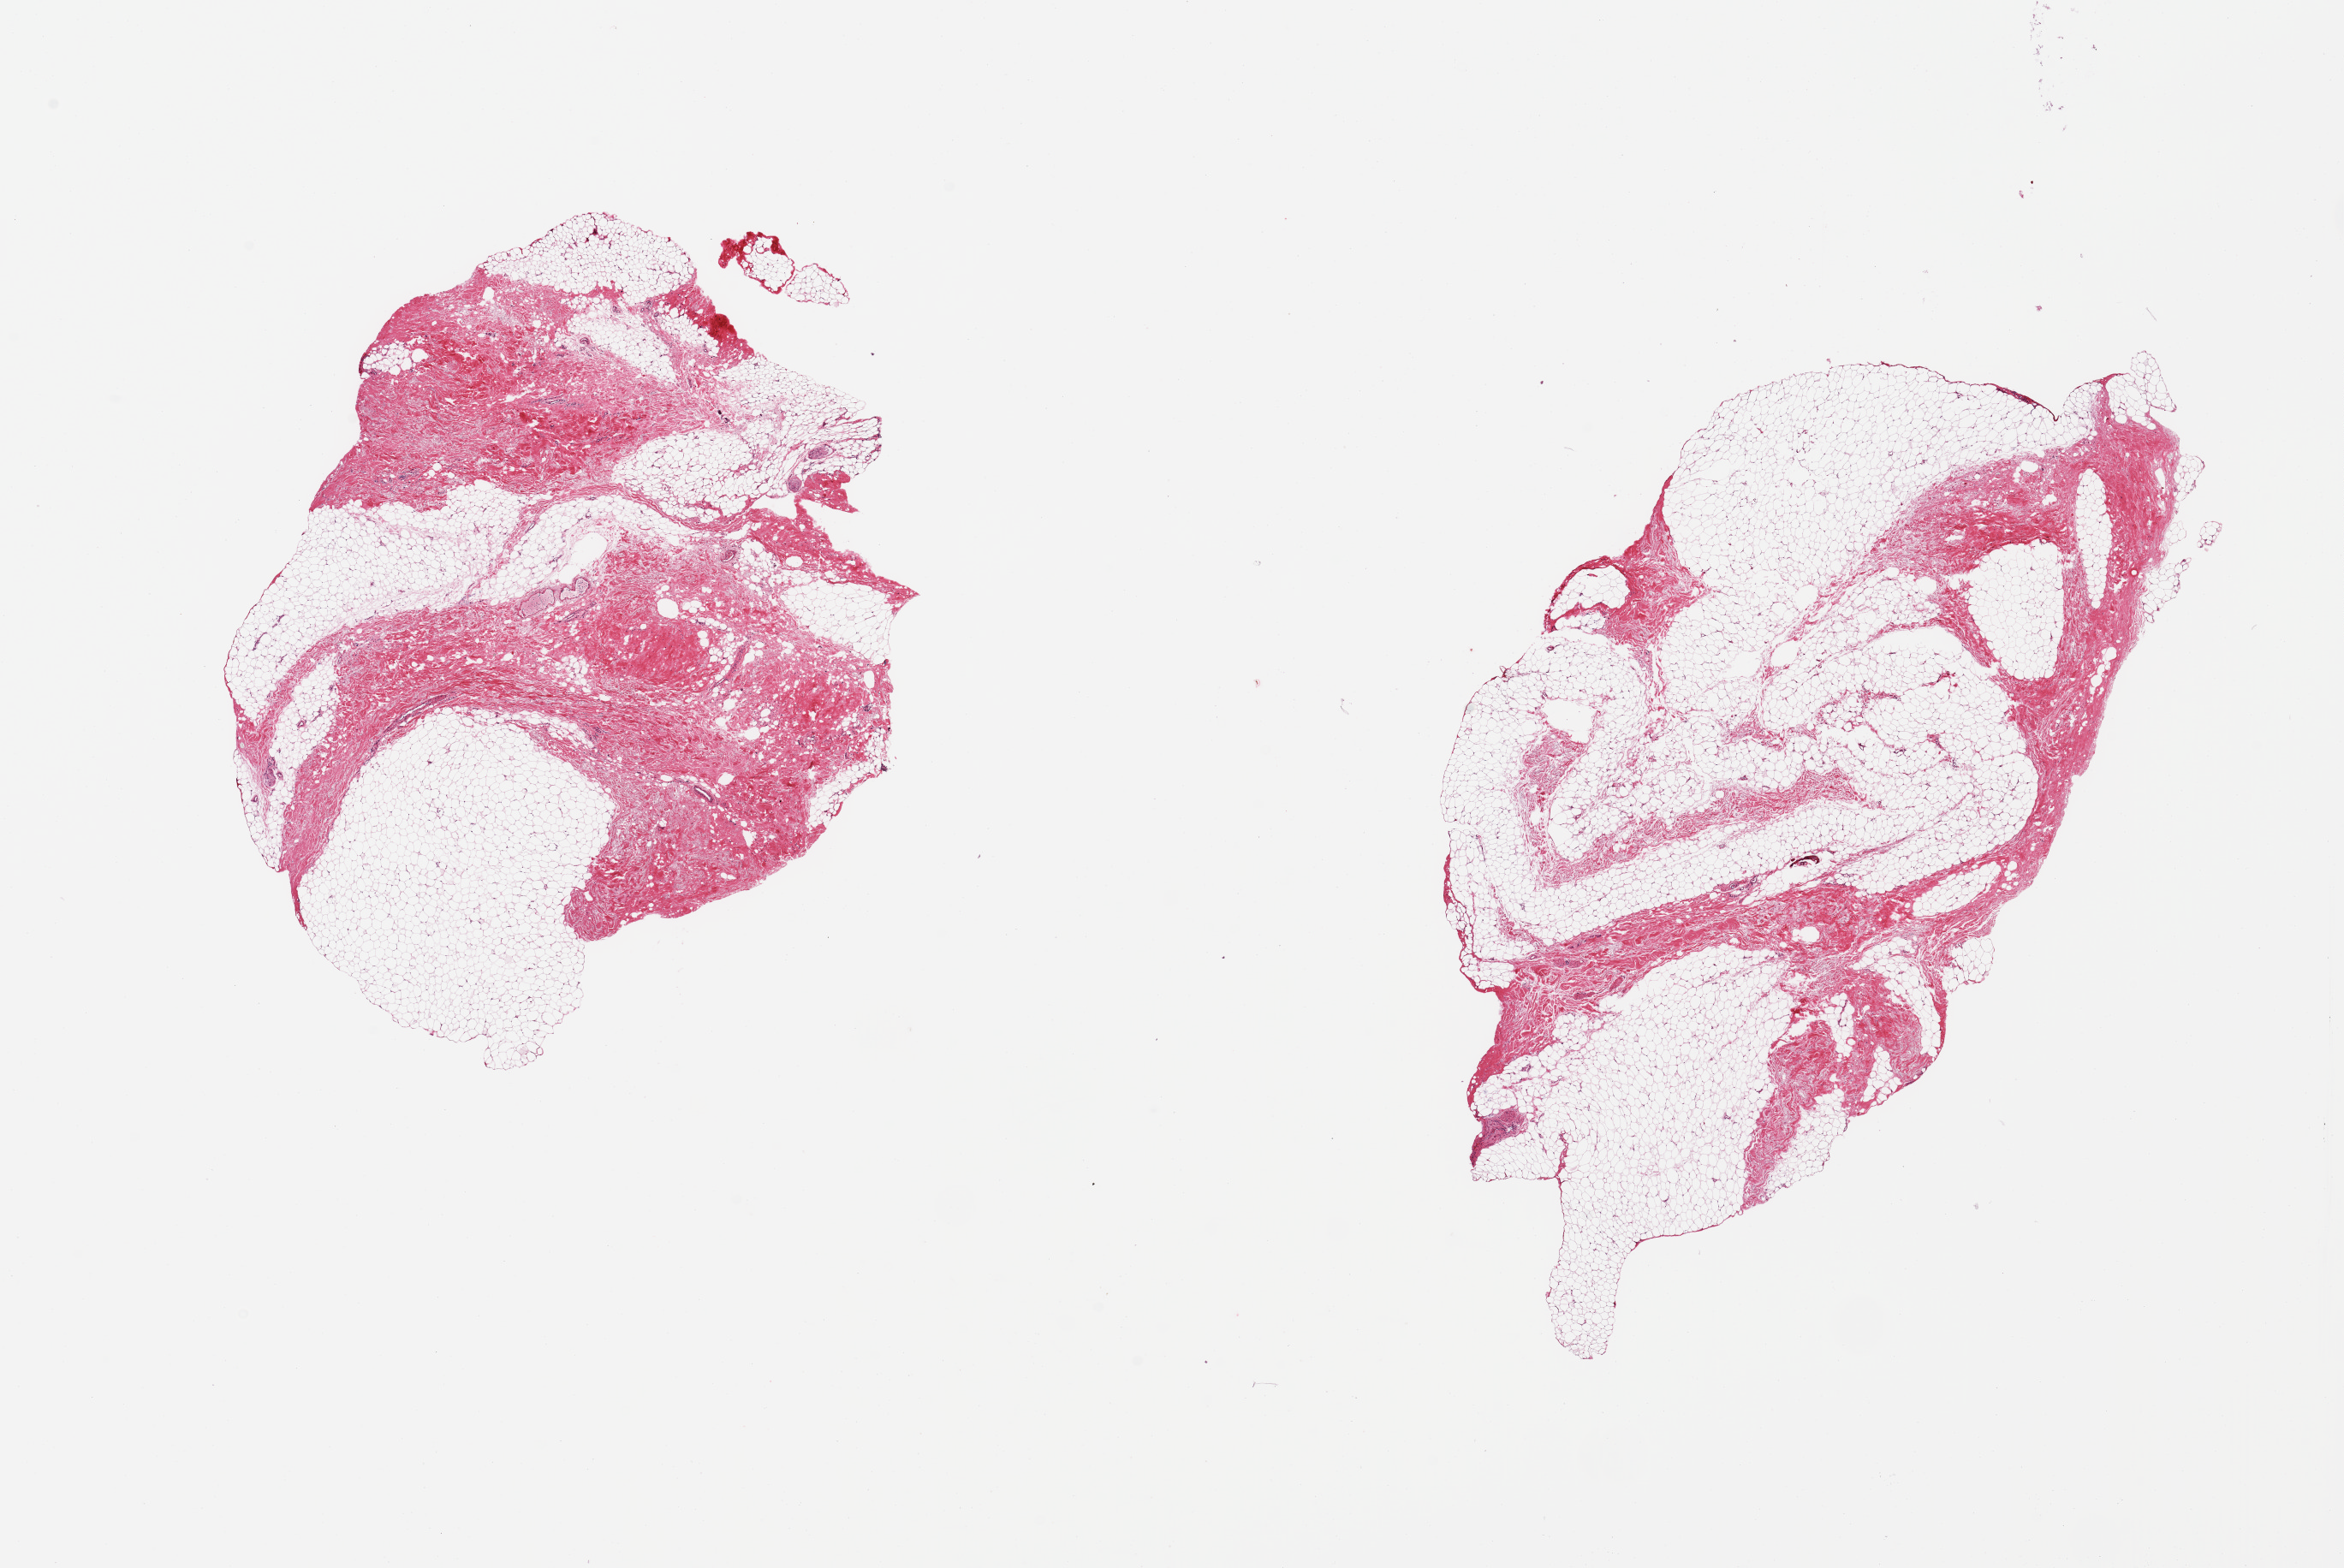
Digitized hematoxylin and eosin (H&E)-stained section, brightfield — shown as a low-resolution overview of the whole scanned area (about 21.7 x 14.5 mm); PAXgene-fixed paraffin-embedded (PFPE) section; sampled site (target tissue): breast; donor tissue sample. Female donor.
Pathologist's review note for this sample: 2 pieces, fibroadipose elements only.